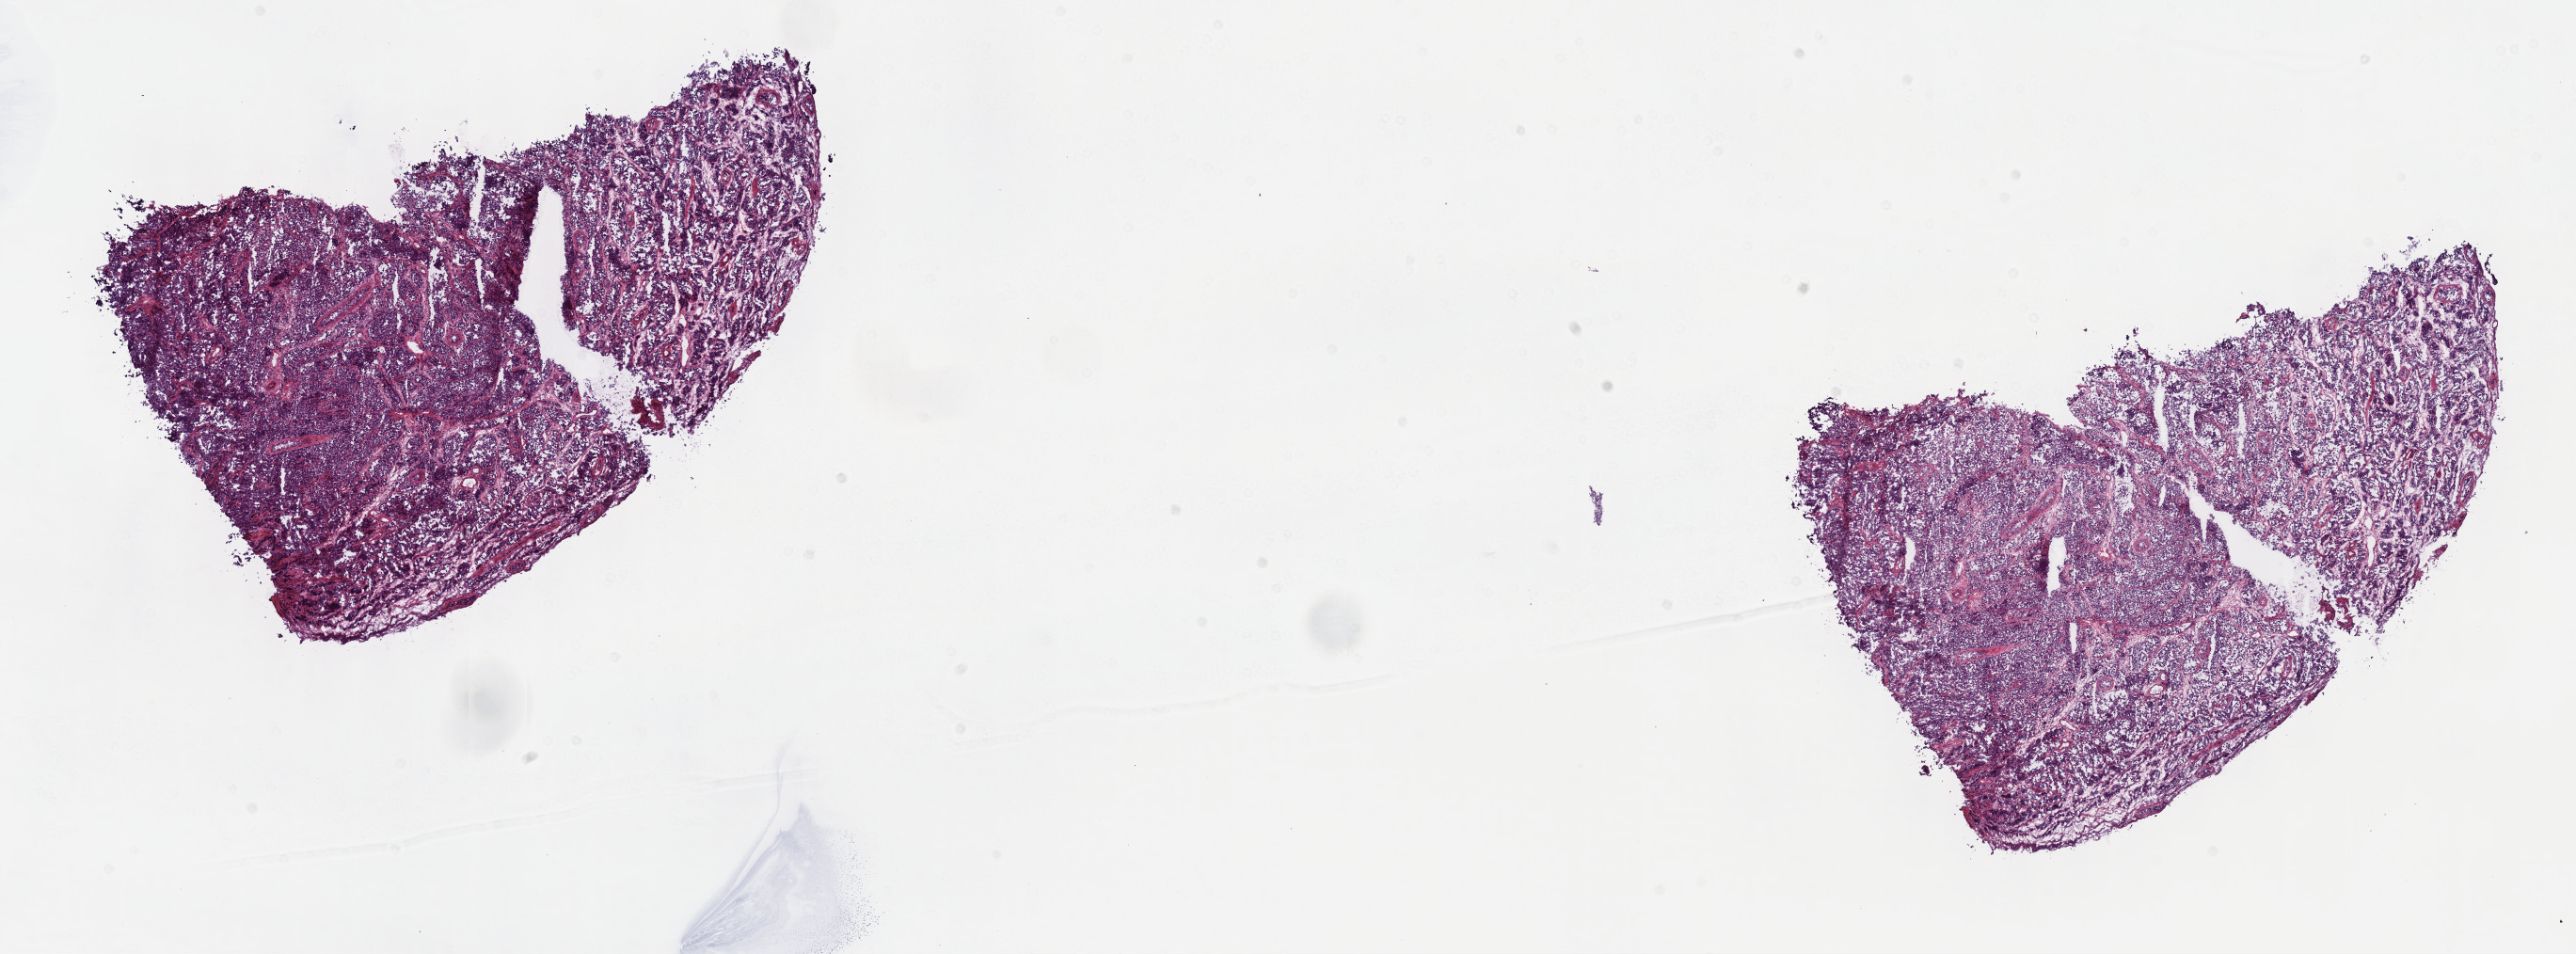
H&E whole-slide image — whole scanned area (about 22.1 x 8.2 mm, slide scanned at 40x) shown as a low-resolution overview. Frozen section. Testis, primary tumour sample. Patient: male, age at initial diagnosis 25 years.
Diagnosis: Seminoma, NOS.